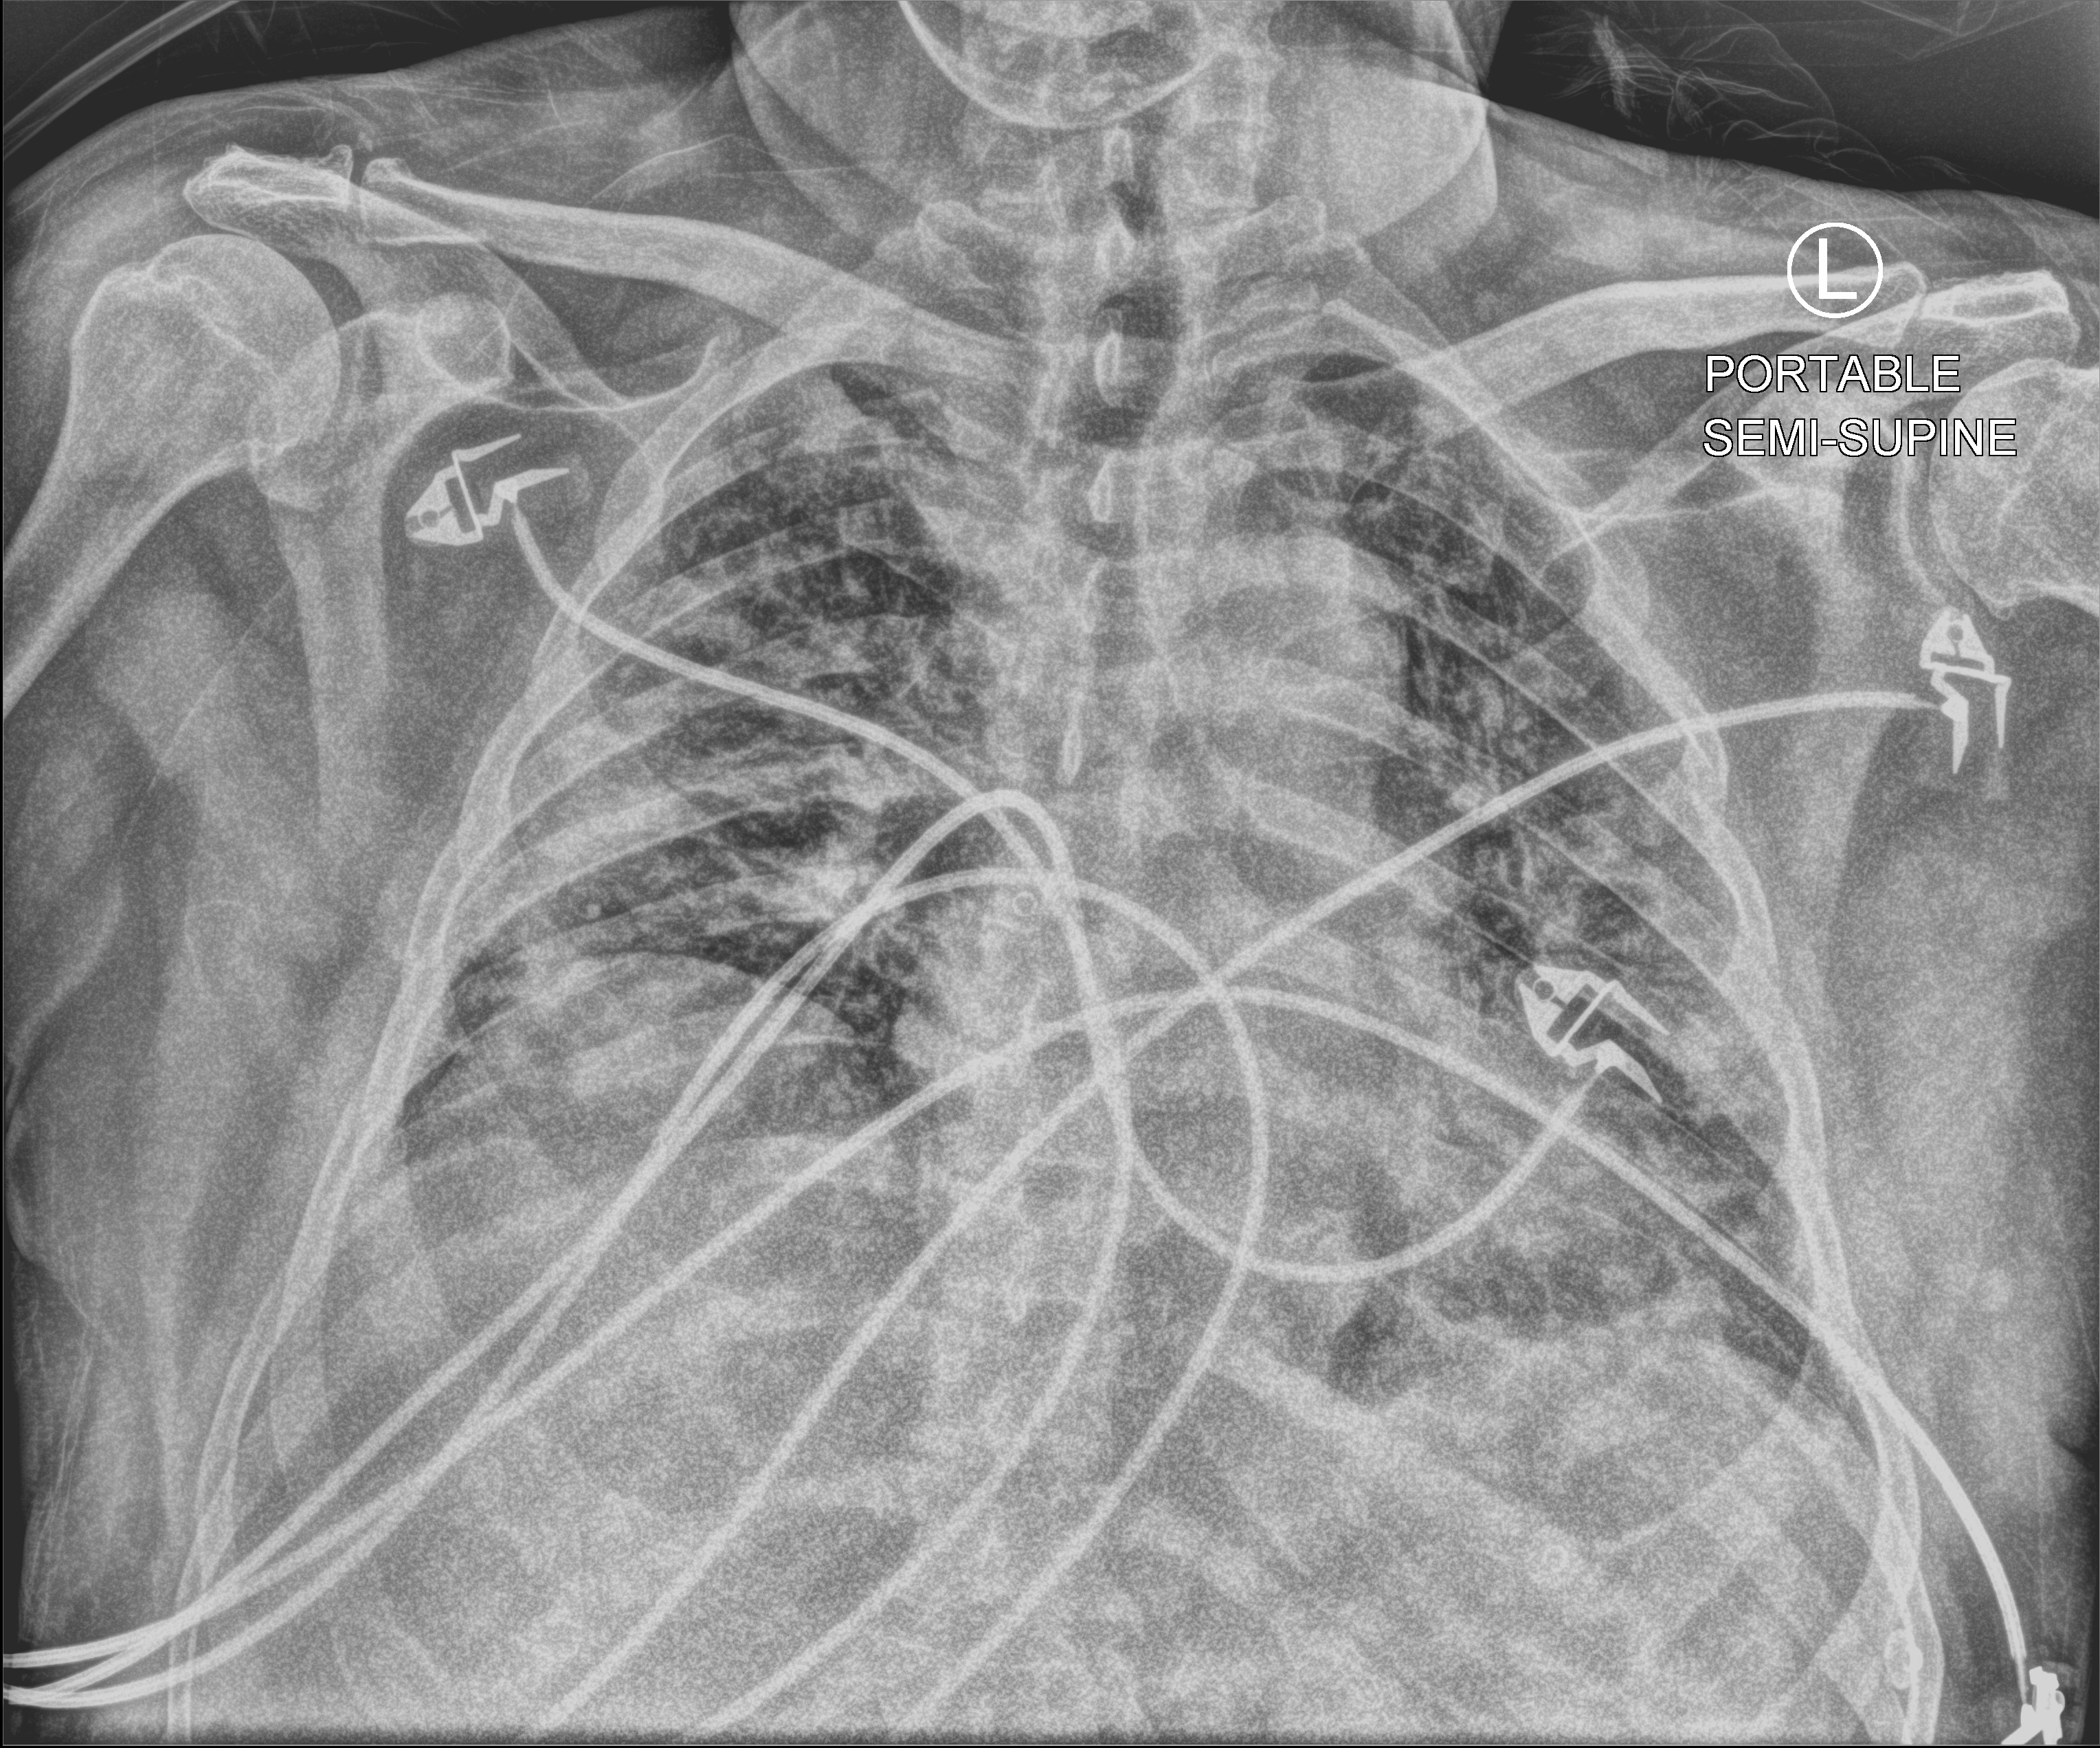
Bedside chest radiograph (computed radiography); anteroposterior (AP) projection. Patient hospitalised with COVID-19; male, aged 60–74 years.
Hospital-stay facts (about this admission, not read from this image; timing relative to this image not recorded):
- hypertension (admission record): yes
- mechanically ventilated during this hospital stay: yes